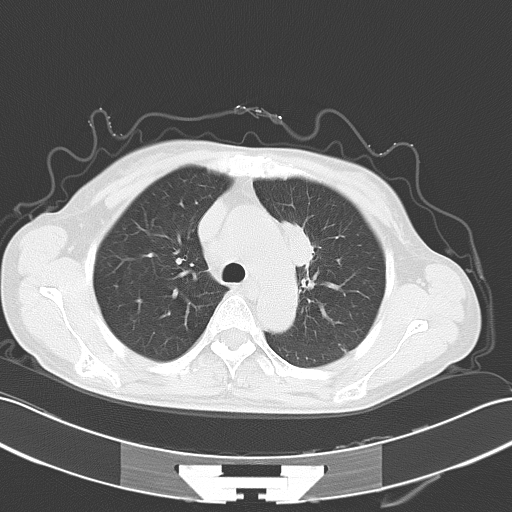
Chest CT, one axial slice; position 40 of 54 along the scan axis; 120 kVp; lung window (W 1500 / L -600 HU); 512 × 512 image matrix, field of view 353 × 353 mm. Female patient, age 50 years. From the clinical record (not read from this slice): clinical TNM (as recorded): T2a N1 M1c.
Annotated regions visible in this slice (rectangle marked by the reading radiologist):
- lung tumour (recorded histology: adenocarcinoma): box from (x=280, y=216) to (x=319, y=274) px